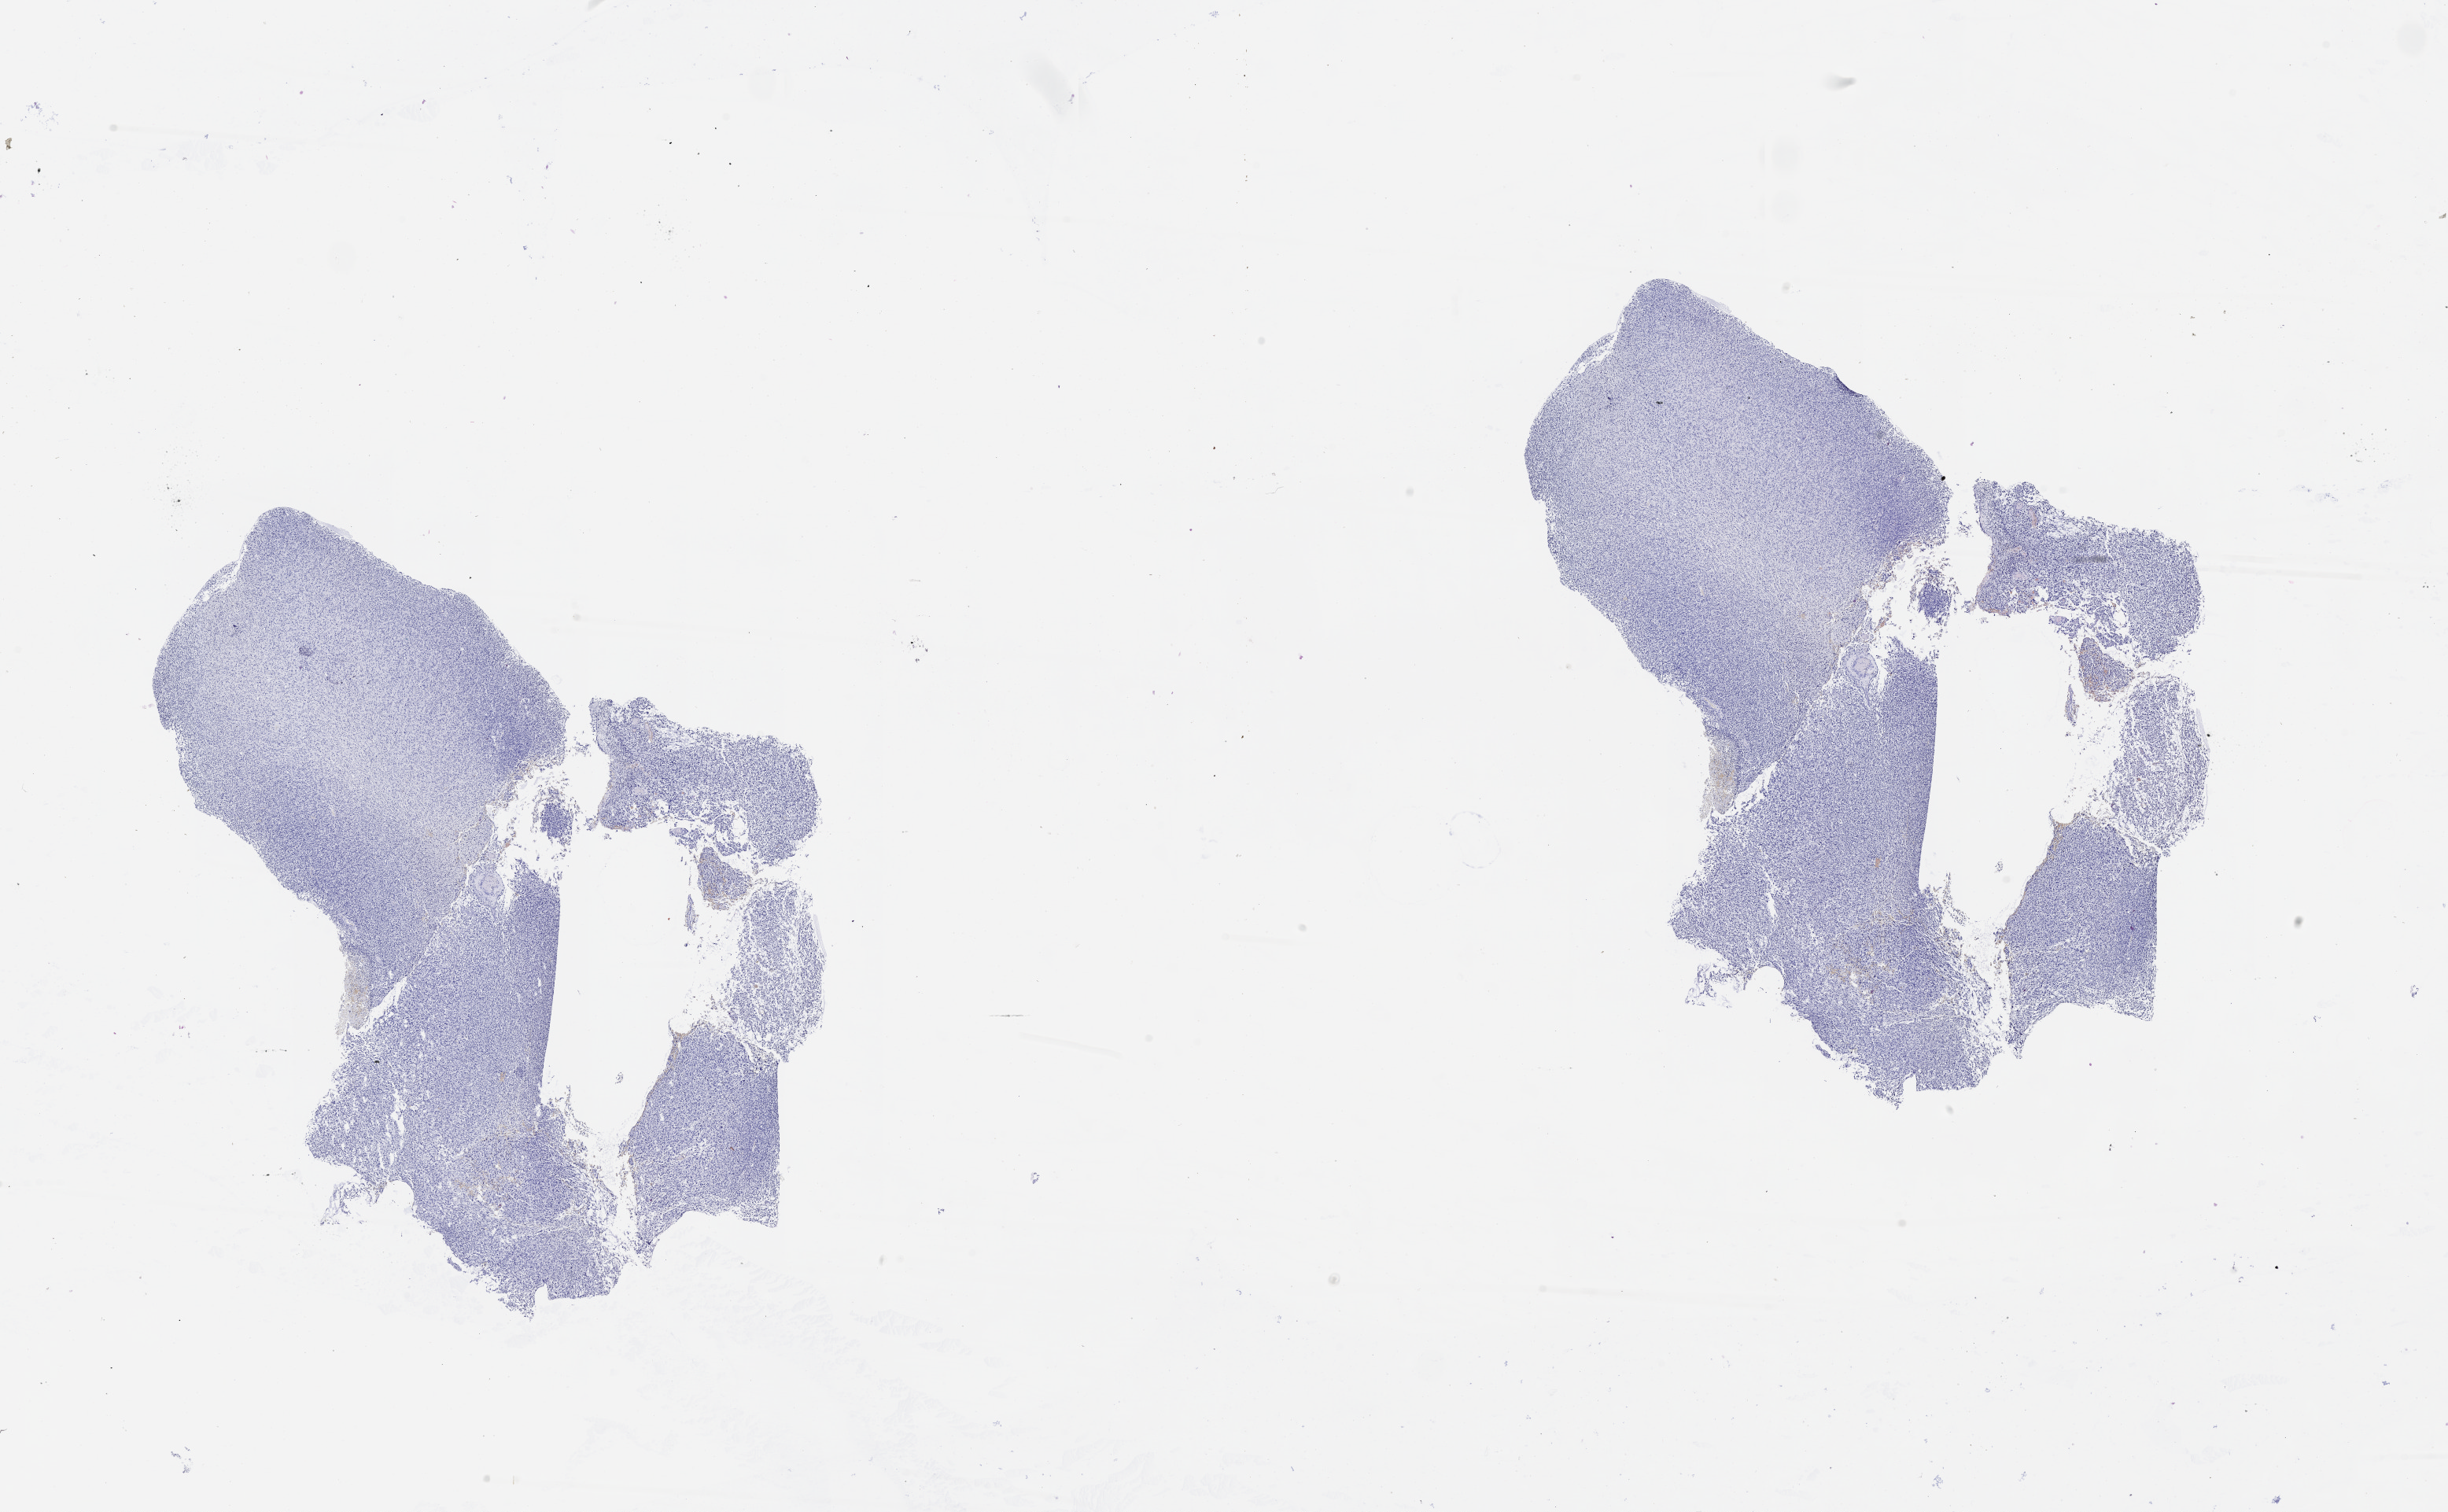
Whole-slide histology image, H&E — low-resolution overview of the scanned area, about 25.1 x 15.5 mm. Tumour tissue sample, sampled site: brain. 36-year-old male patient. Slide review estimates, as recorded: tumour nuclei 90%, necrosis 3%.
• diagnosis: Glioblastoma
• primary tumour site (as recorded): frontal lobe